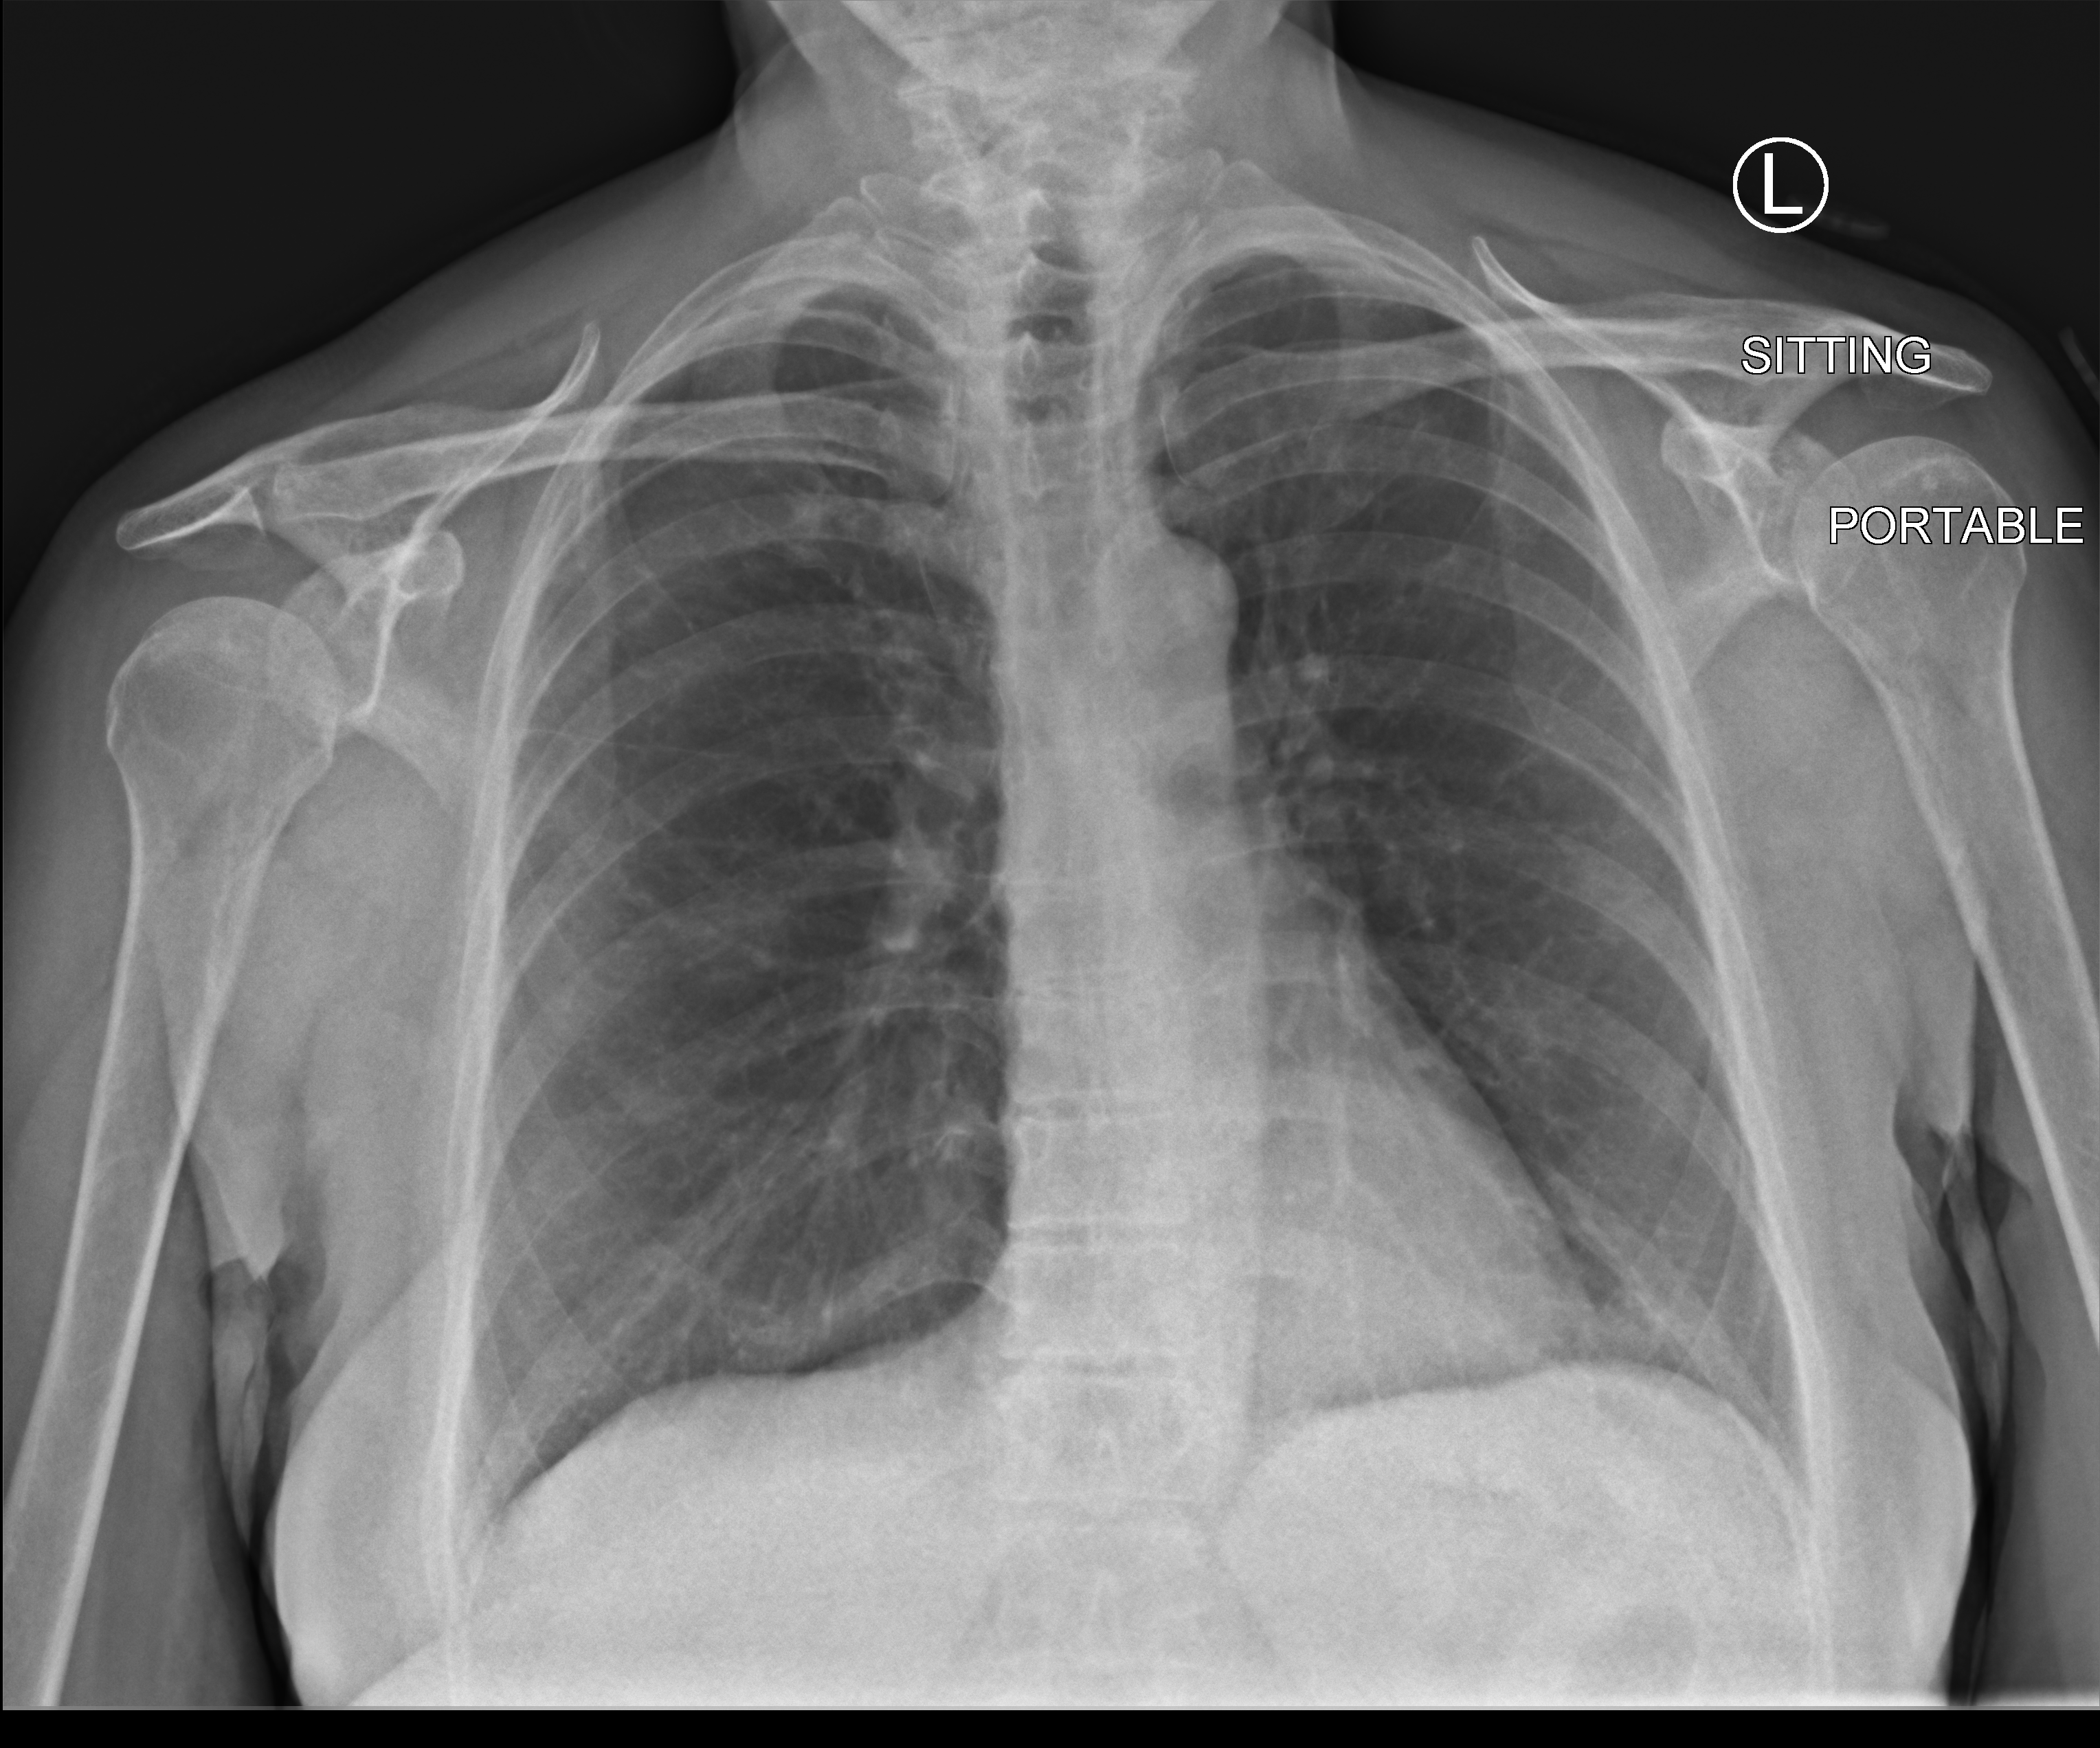
Chest X-ray (portable), anteroposterior (AP) projection. Patient hospitalised with COVID-19; female, aged 60–74 years.
From the hospital-stay record, not from the radiograph (when in the stay this image was taken is not recorded):
- mechanically ventilated during this hospital stay: no